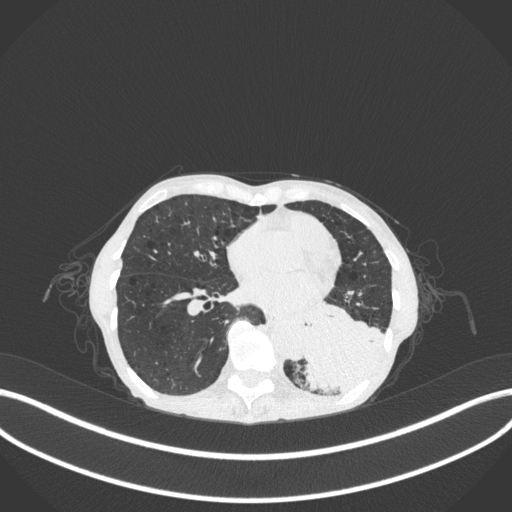
Chest CT, one axial slice; position 104 of 347 along the scan axis; reconstruction kernel B31f; 120 kVp; lung window (W 1500 / L -600 HU); 512 × 512 image matrix, field of view 400 × 400 mm. Female patient, age 70 years. Case-level facts recorded for this patient, not image findings: clinical TNM (as recorded): T3 N0 M0; histopathological grade: G3.
Annotated regions visible in this slice (bounding box drawn by a radiologist):
- lung tumour (recorded histology: small cell carcinoma): box from (x=290, y=290) to (x=391, y=398) px